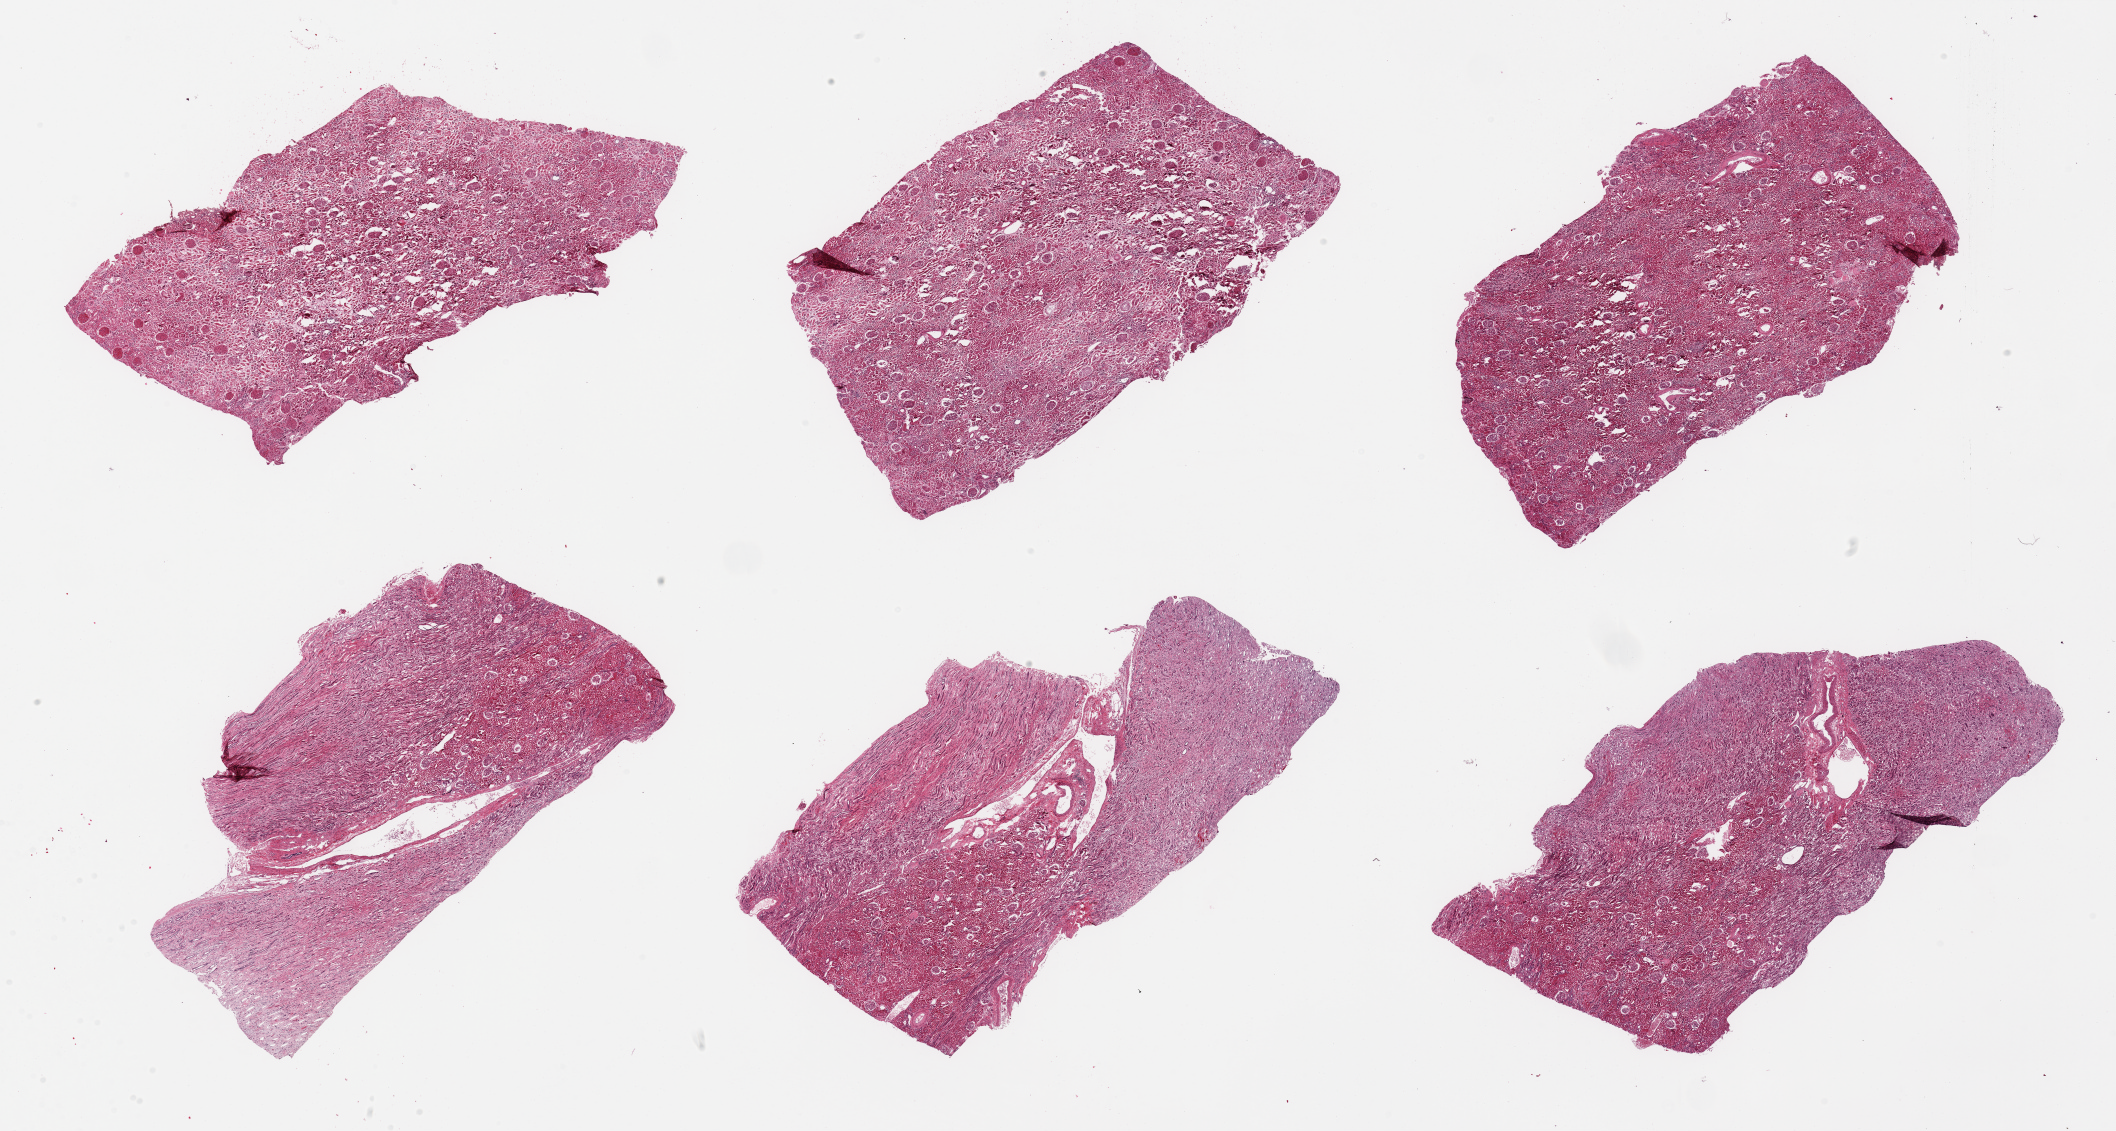
Digitized hematoxylin and eosin (H&E)-stained section, brightfield — low-resolution overview of the scanned area, about 33.5 x 17.9 mm. PAXgene-fixed, paraffin-embedded tissue. Sampled site (target tissue): renal cortex. Tissue donor sample. Female donor.
Review note (as recorded): 6 pieces; includes significant portion of medulla (30%), some sclerotic glomeruli.